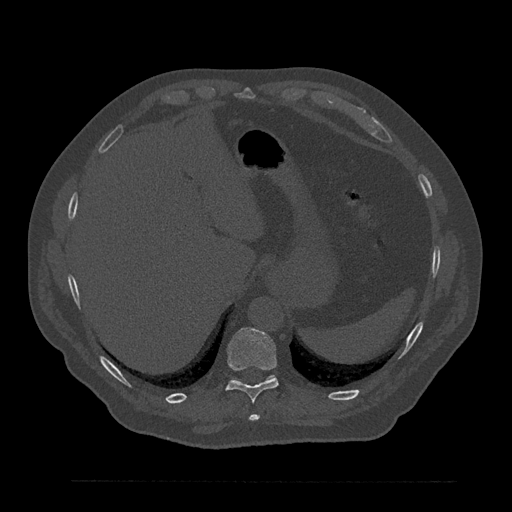
CT including the spine, one axial slice; slice 340 of 797 in the series (ordered by position); reconstruction kernel Br40s/3; bone window (W 1800 / L 400 HU); 0.5 mm slice thickness; 512 × 512 image matrix, field of view 430 × 430 mm. Patient: male, 61 years. Case-level facts recorded for this patient, not image findings: primary cancer: prostate.
Outlined on this slice (semi-automatic segmentation, software-assisted and operator-edited):
- T10 vertebra: bounding box (x1, y1, x2, y2) in pixels: (226, 328, 278, 403)
- T11 vertebra: (234, 379, 268, 381)
- T9 vertebra: (249, 414, 260, 421)